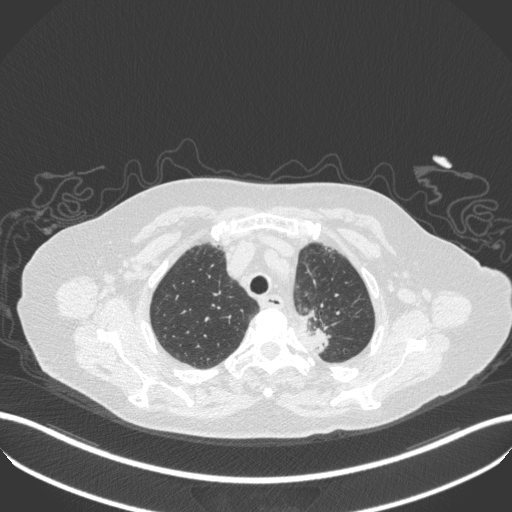
Chest CT, one axial slice; slice 280 of 353 in the series (ordered by position); 100 kVp; lung window (W 1500 / L -600 HU); 1 mm slice thickness; 512 × 512 image matrix. Female patient, age 81 years. From the clinical record (not read from this slice): clinical TNM (as recorded): T2a N0 M0.
Annotated regions visible in this slice (rectangle marked by the reading radiologist):
- lung tumour (recorded histology: adenocarcinoma): bounding box <290,304,338,359> (left, top, right, bottom; pixels)